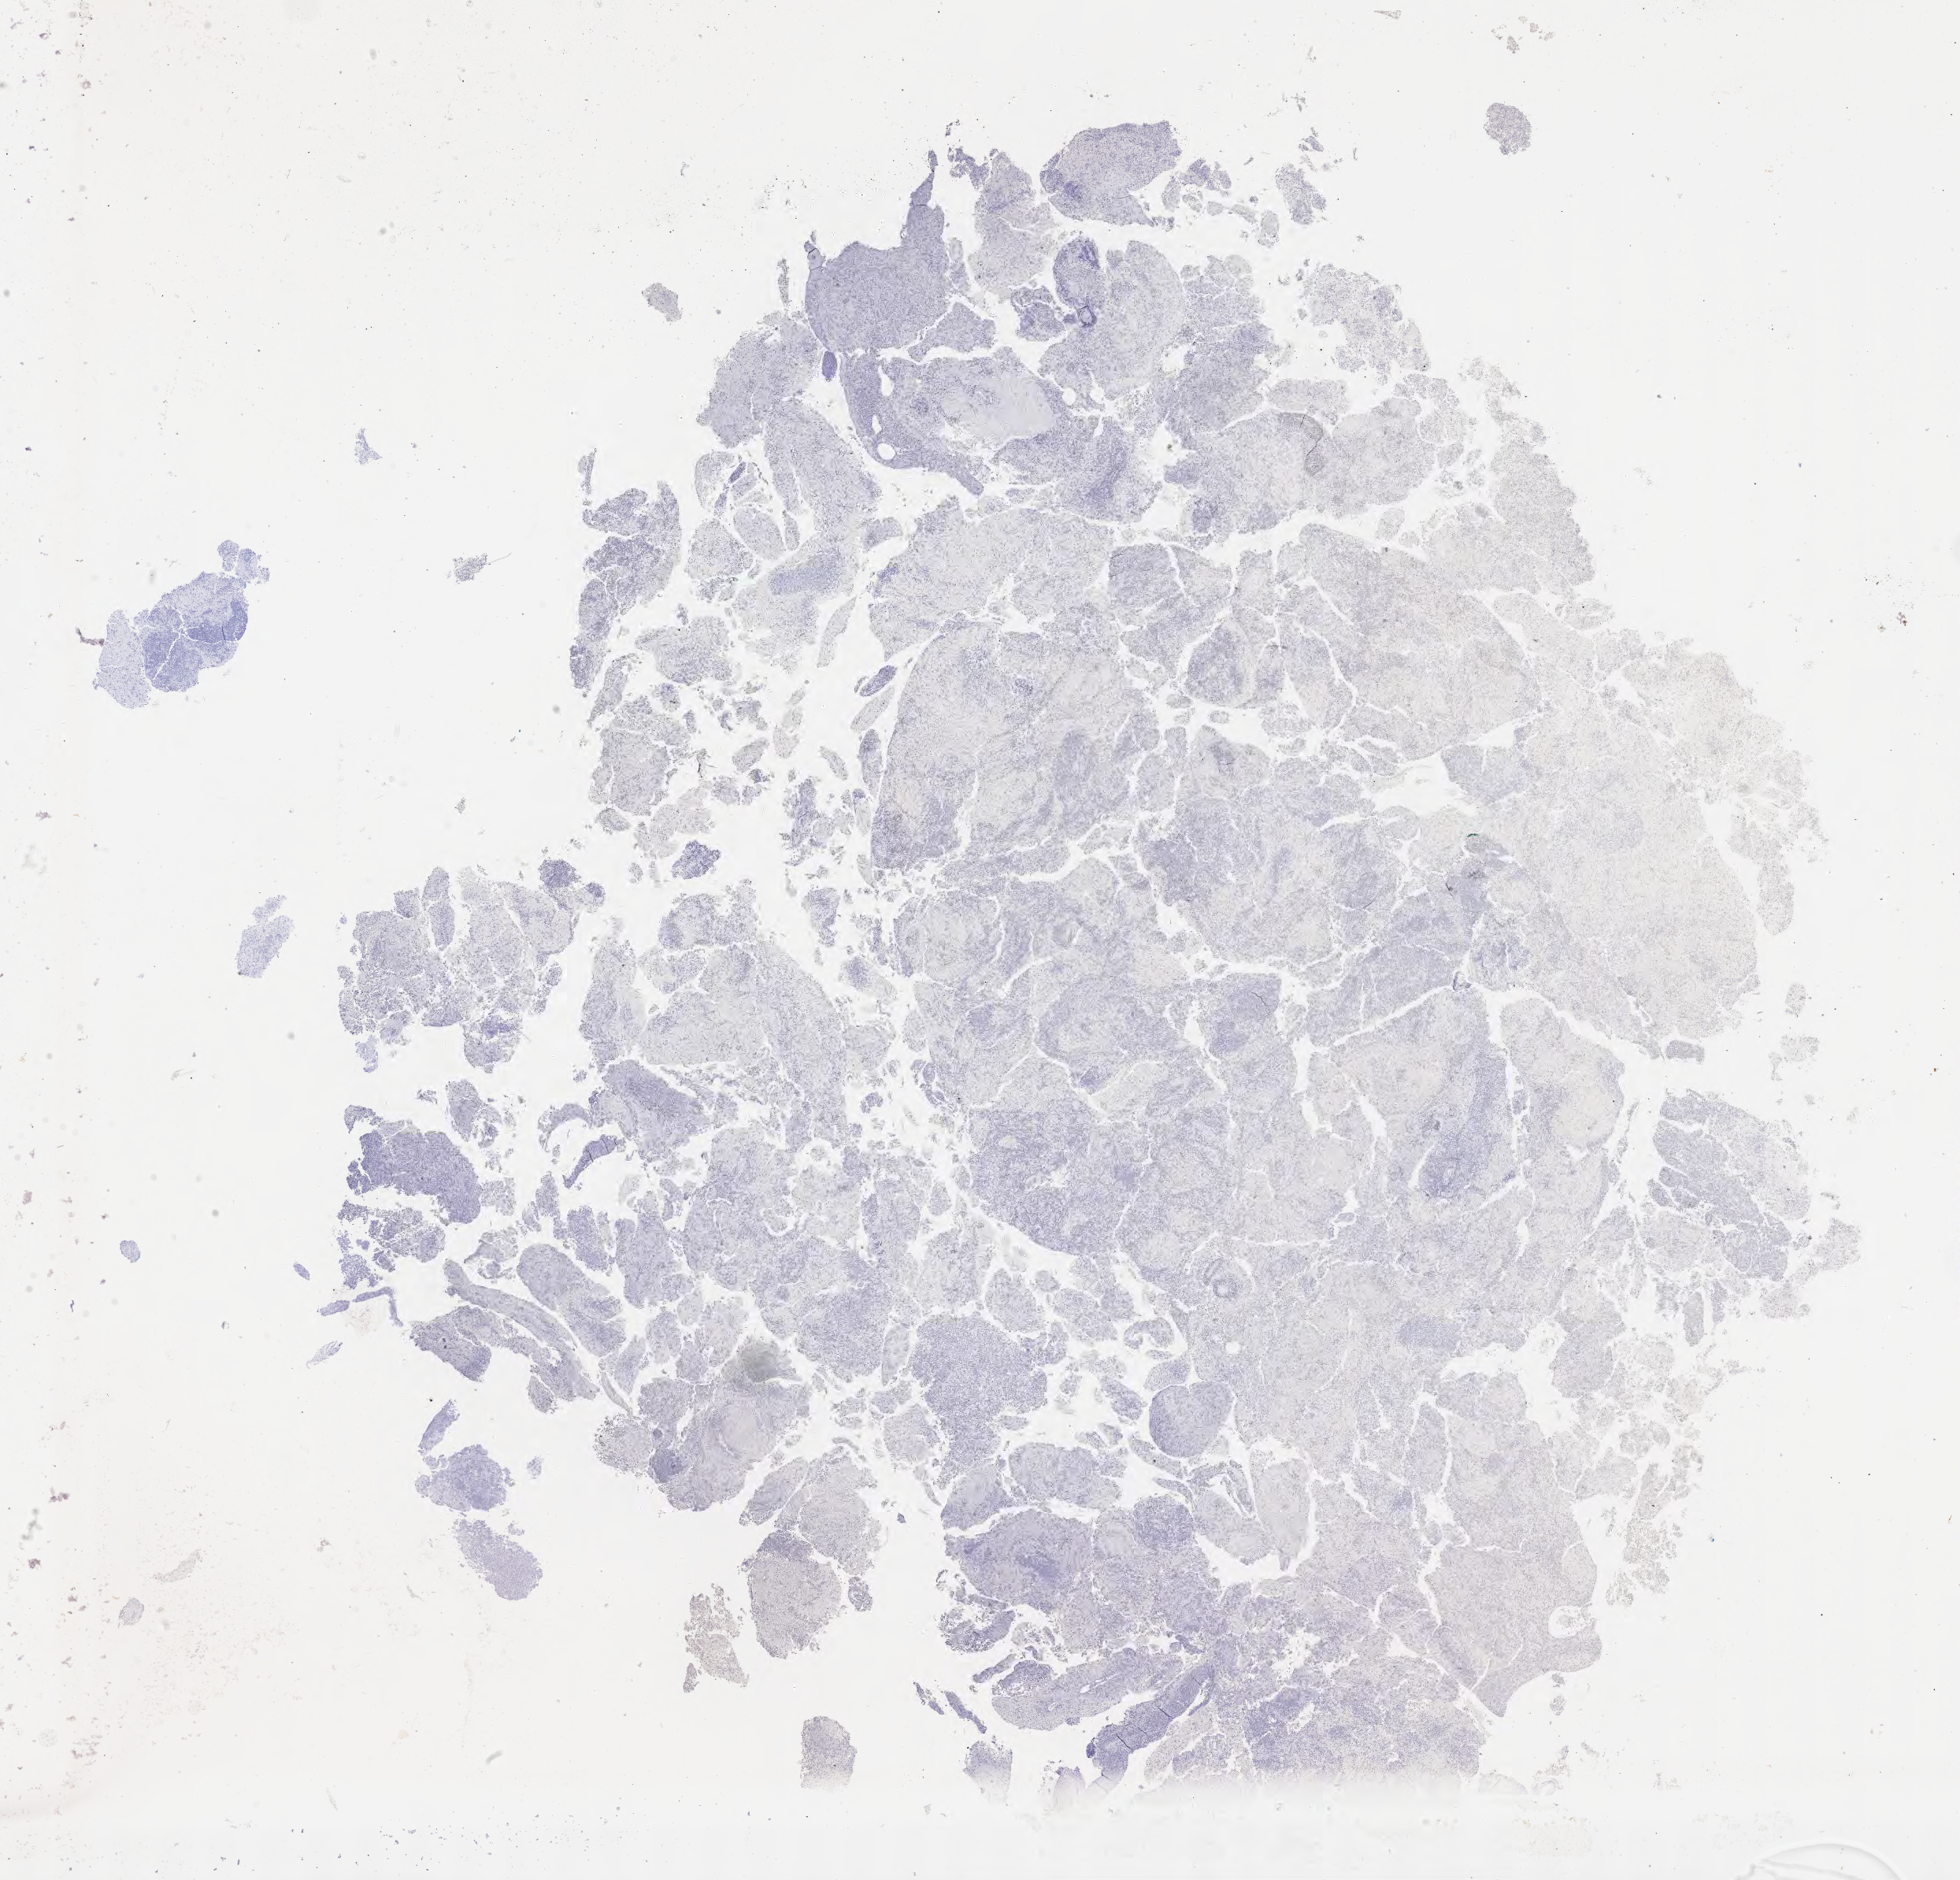
Immunohistochemistry (IHC) whole-slide image stained for p53, shown as a low-resolution overview of the whole scanned area (about 20.1 x 19.3 mm); tumor tissue; site: brain. Patient: male, aged 51.
Diagnosis: Diffuse large B-cell lymphoma, NOS.